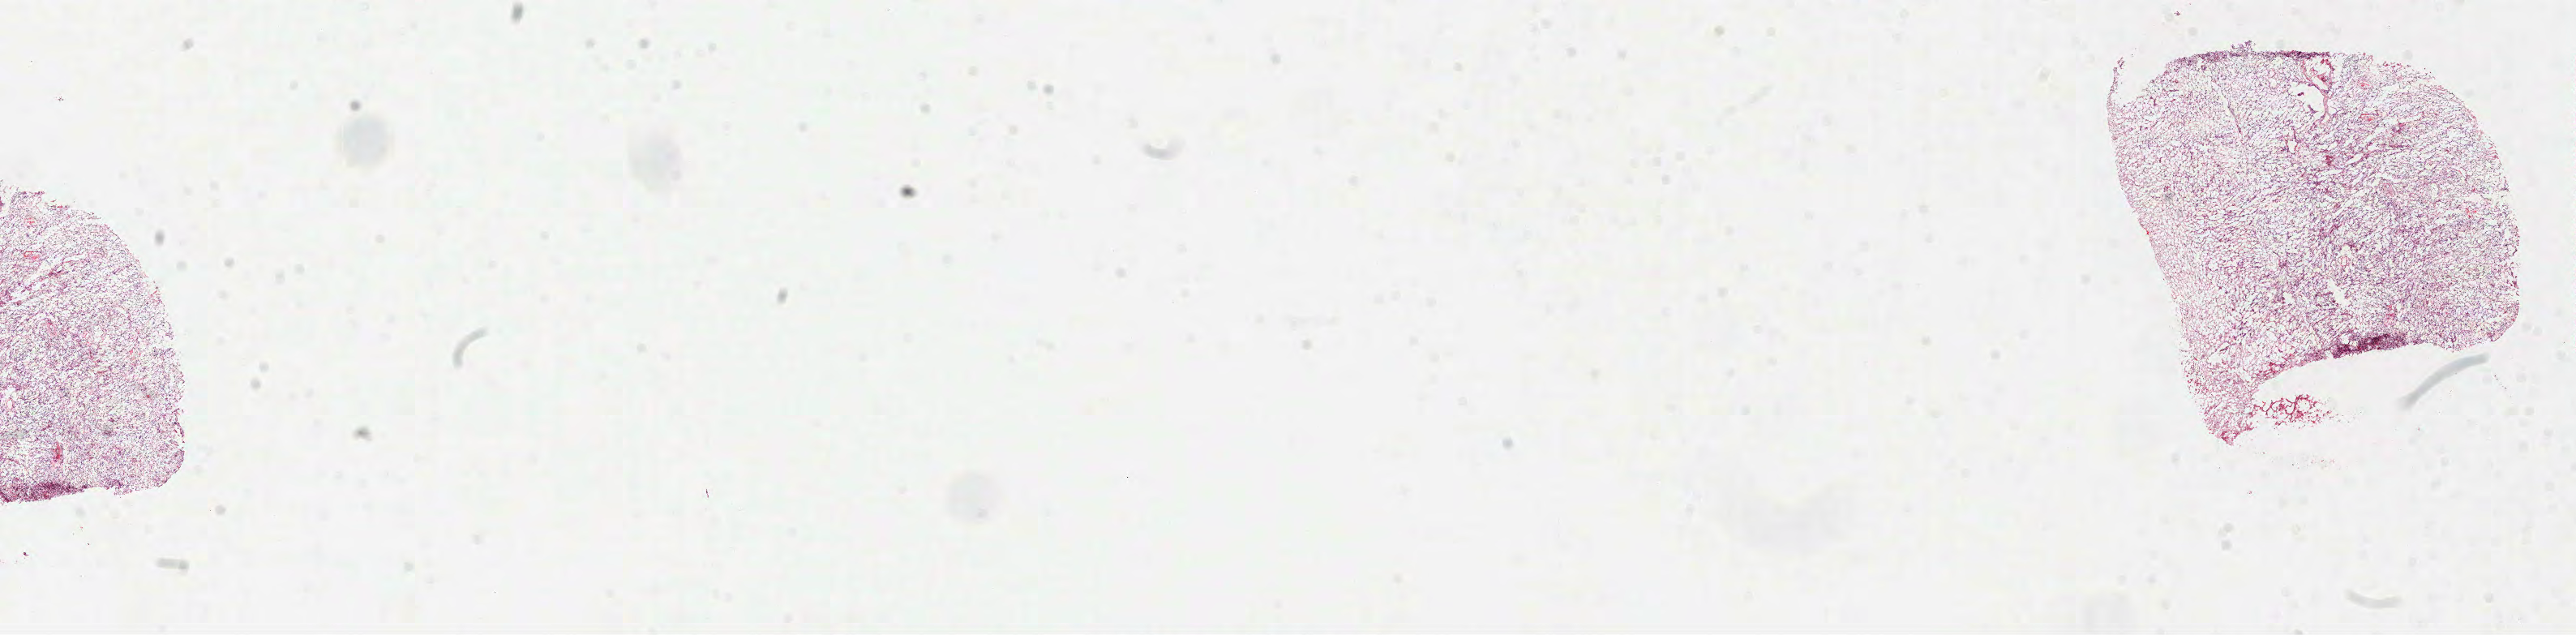
Whole-slide histology image, Hematoxylin and eosin (H&E) stained — low-resolution overview of the scanned area, about 25.6 x 6.3 mm (acquisition: 40x scan). Formalin-fixed paraffin-embedded (FFPE) diagnostic section. Primary tumour sample from the brain. Patient: male, age at initial diagnosis 36 years.
Diagnosis: Glioblastoma.